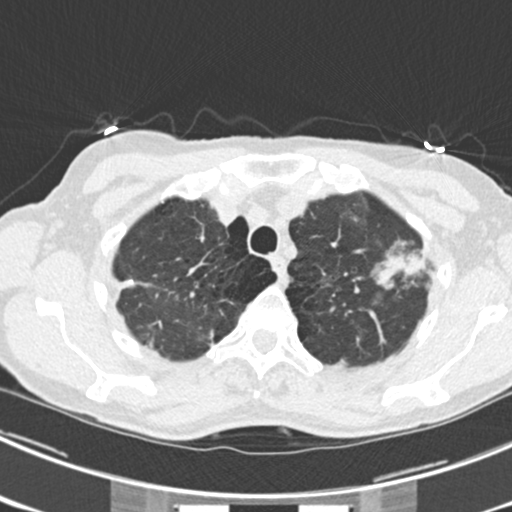
Chest CT (low-dose screening protocol), one axial image; third screening round (two years after baseline); lung window (W 1500 / L -600 HU); standard (soft-tissue) reconstruction kernel (B30f); 120 kVp. Female participant, aged 63 years at enrolment. Current smoker at enrolment.
• Lesion marked by an expert reader, bounding box (x1, y1, x2, y2) in pixels: (374, 235, 442, 297).
• The screening reader recorded 9 non-calcified nodules or masses ≥4 mm on this exam (left upper lobe, right upper lobe, left upper lobe, left lower lobe, right middle lobe, left lower lobe, left lower lobe, right lower lobe, right lower lobe); which of them this box marks is not recorded.
• Official screen result: positive, other.
• Later outcome: lung cancer diagnosed 15 days after this screen — bronchiolo-alveolar adenocarcinoma, NOS, right upper lobe, right middle lobe, right lower lobe, left upper lobe, left lower lobe, moderately differentiated (G2), stage IV (AJCC 6th edition).